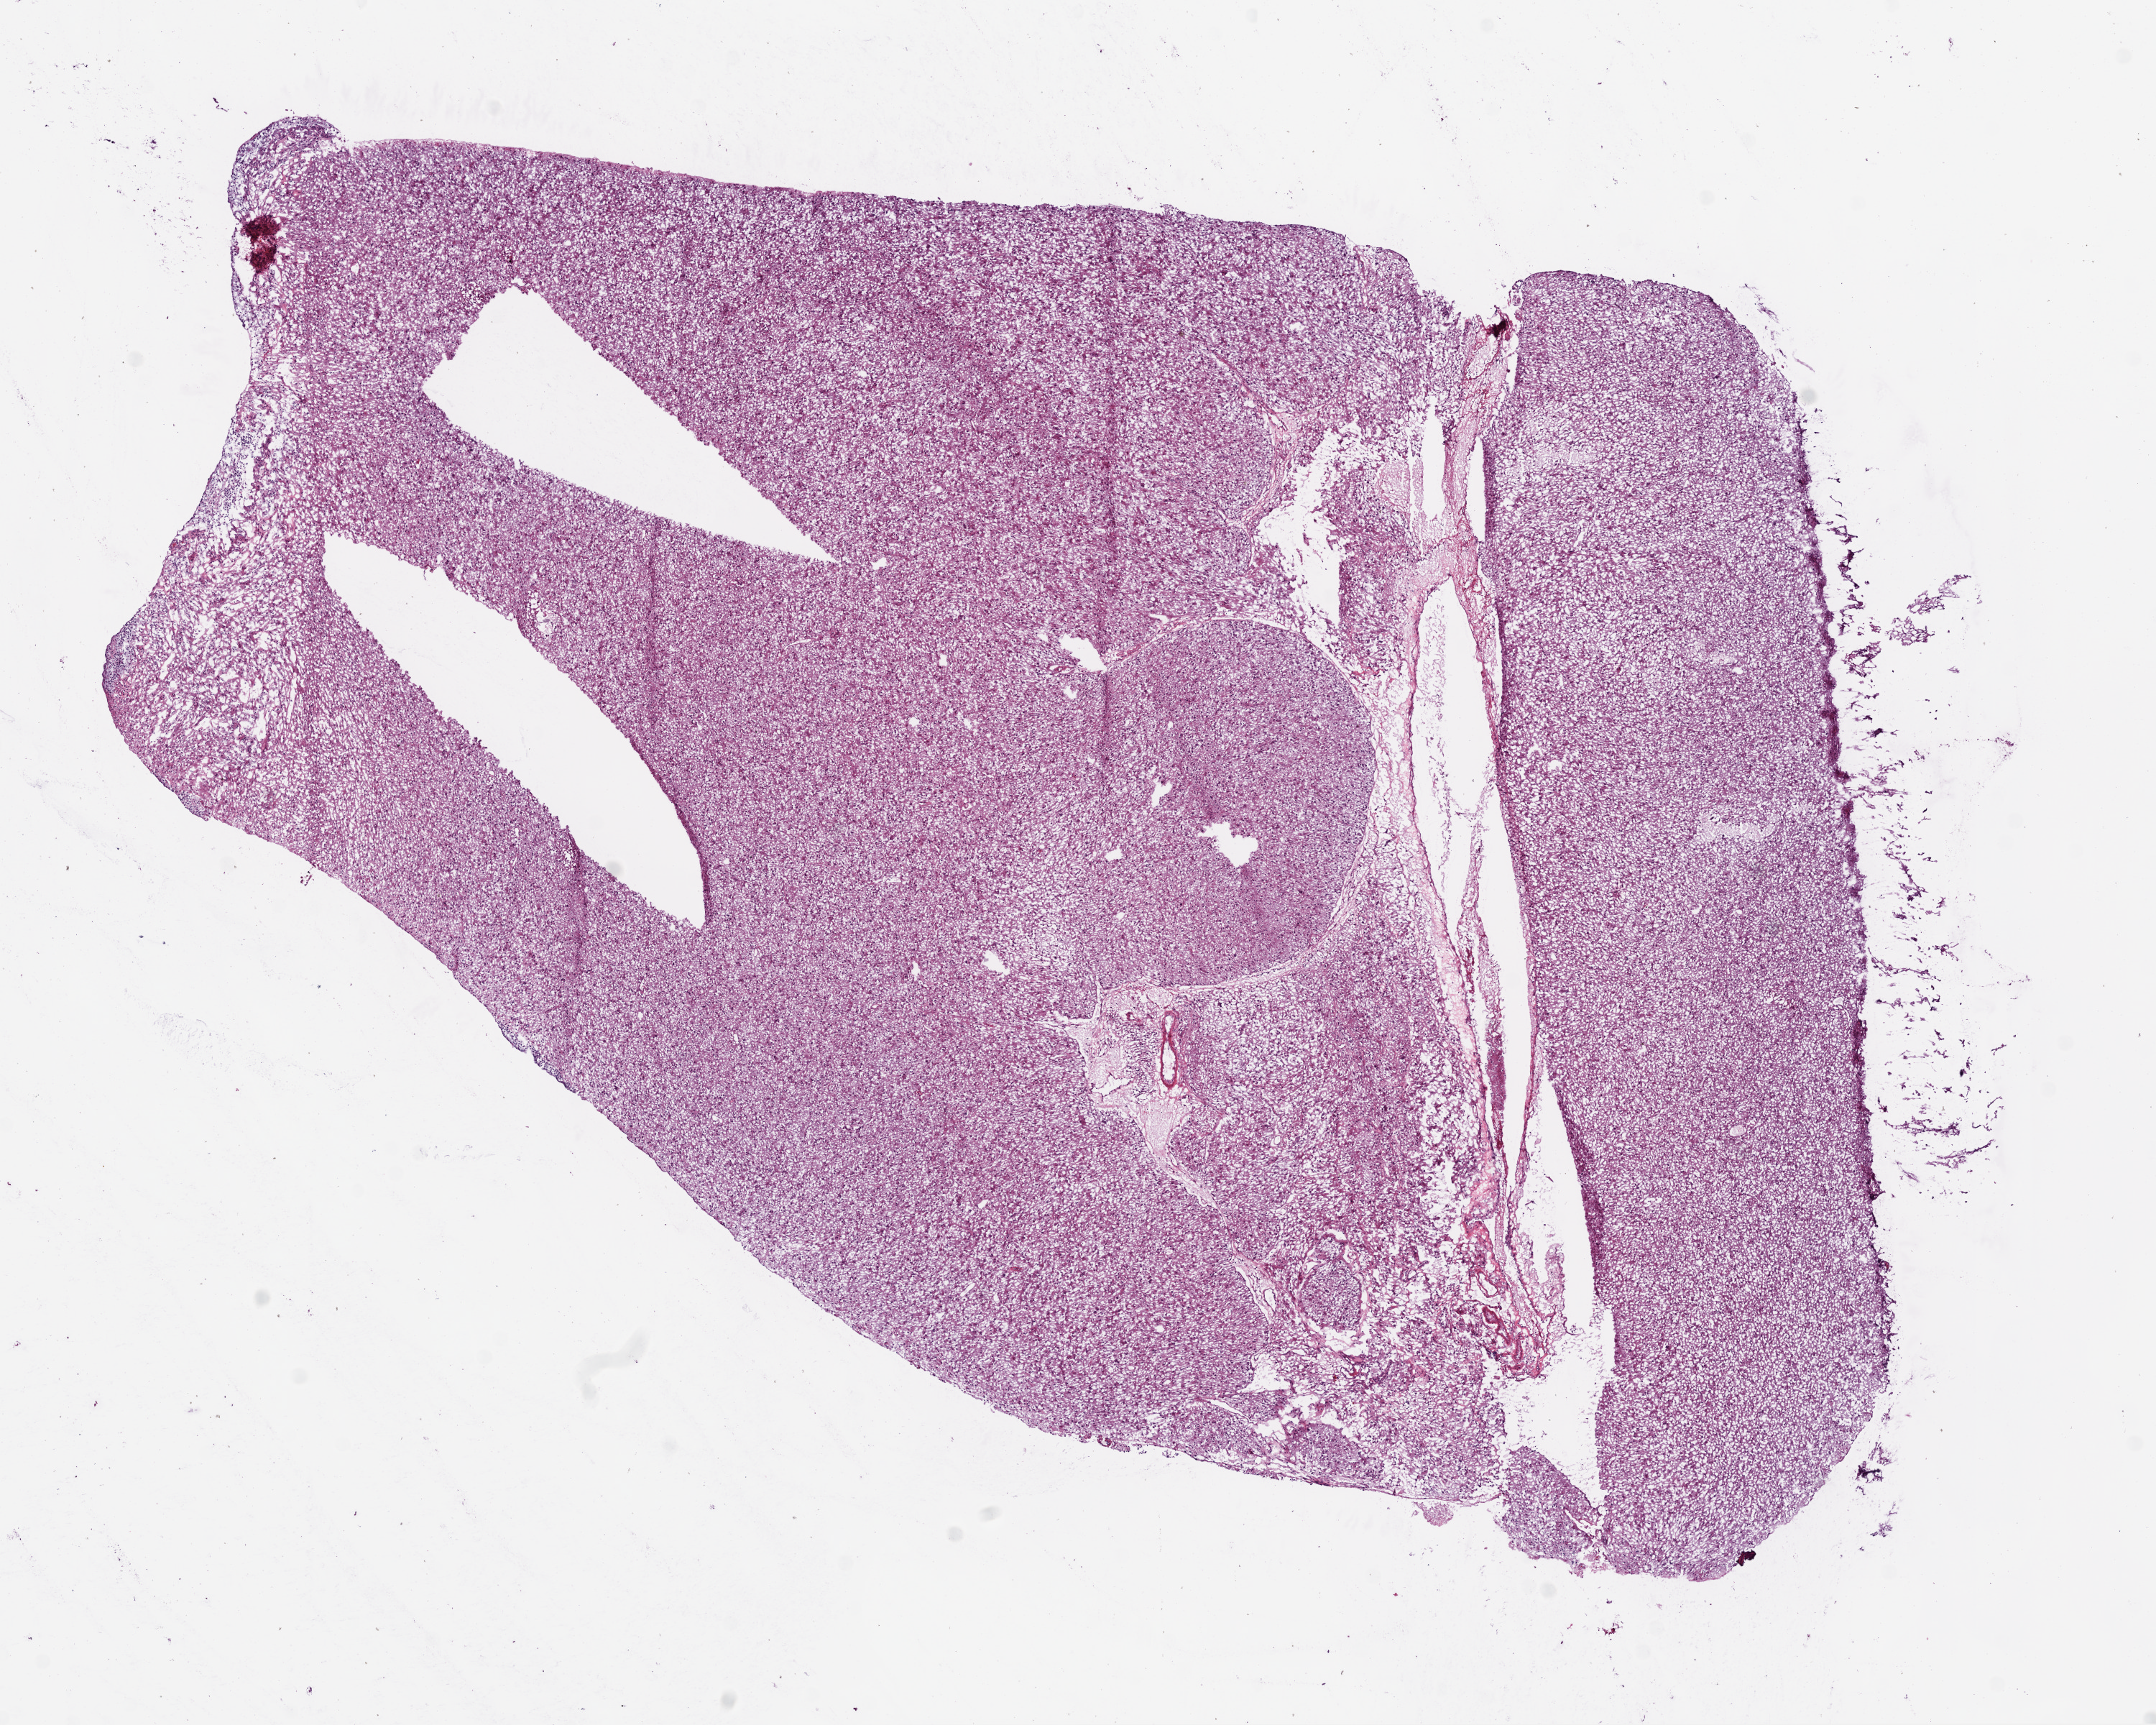
Whole-slide histology image, Hematoxylin and eosin (H&E) stained — whole scanned area (about 12.0 x 9.6 mm, acquisition: 20x scan) shown as a low-resolution overview; frozen section from the bottom of the tissue portion; primary tumour sample from the brain. Male patient; age at initial diagnosis 76 years. Pathologist review of this section (percent, as recorded): tumour cells 100%, tumour nuclei 80%.
Histologic diagnosis: Glioblastoma.